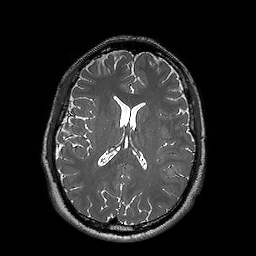
Brain MRI from a brain-tumour surgery series, one axial slice. Slice 76 of 192 in the series (ordered by position). 256 × 256 image matrix, field of view 250 × 250 mm. Case-level facts recorded for this patient, not image findings: histopathology: Oligodendroglioma; WHO grade: 2.
Annotated regions visible in this slice (outlined manually by an expert reader):
- tumour: bounding box <170,166,189,182> (left, top, right, bottom; pixels)